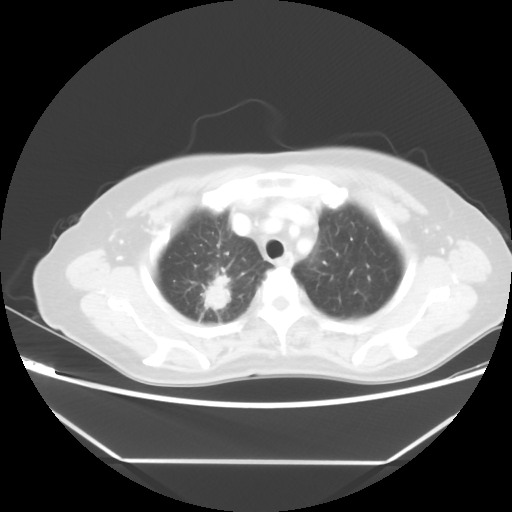
Chest CT, one axial slice; position 41 of 48 along the scan axis; reconstruction kernel STANDARD; 100 kVp; lung window (W 1500 / L -600 HU); 5 mm slice thickness; 512 × 512 image matrix, field of view 360 × 360 mm. Female patient, age 65 years. Case-level facts recorded for this patient, not image findings: clinical TNM (as recorded): T1c N1 M1.
Outlined on this slice (rectangle marked by the reading radiologist):
- lung tumour (recorded histology: adenocarcinoma): bounding box [x1, y1, x2, y2] px = [199, 269, 240, 325]